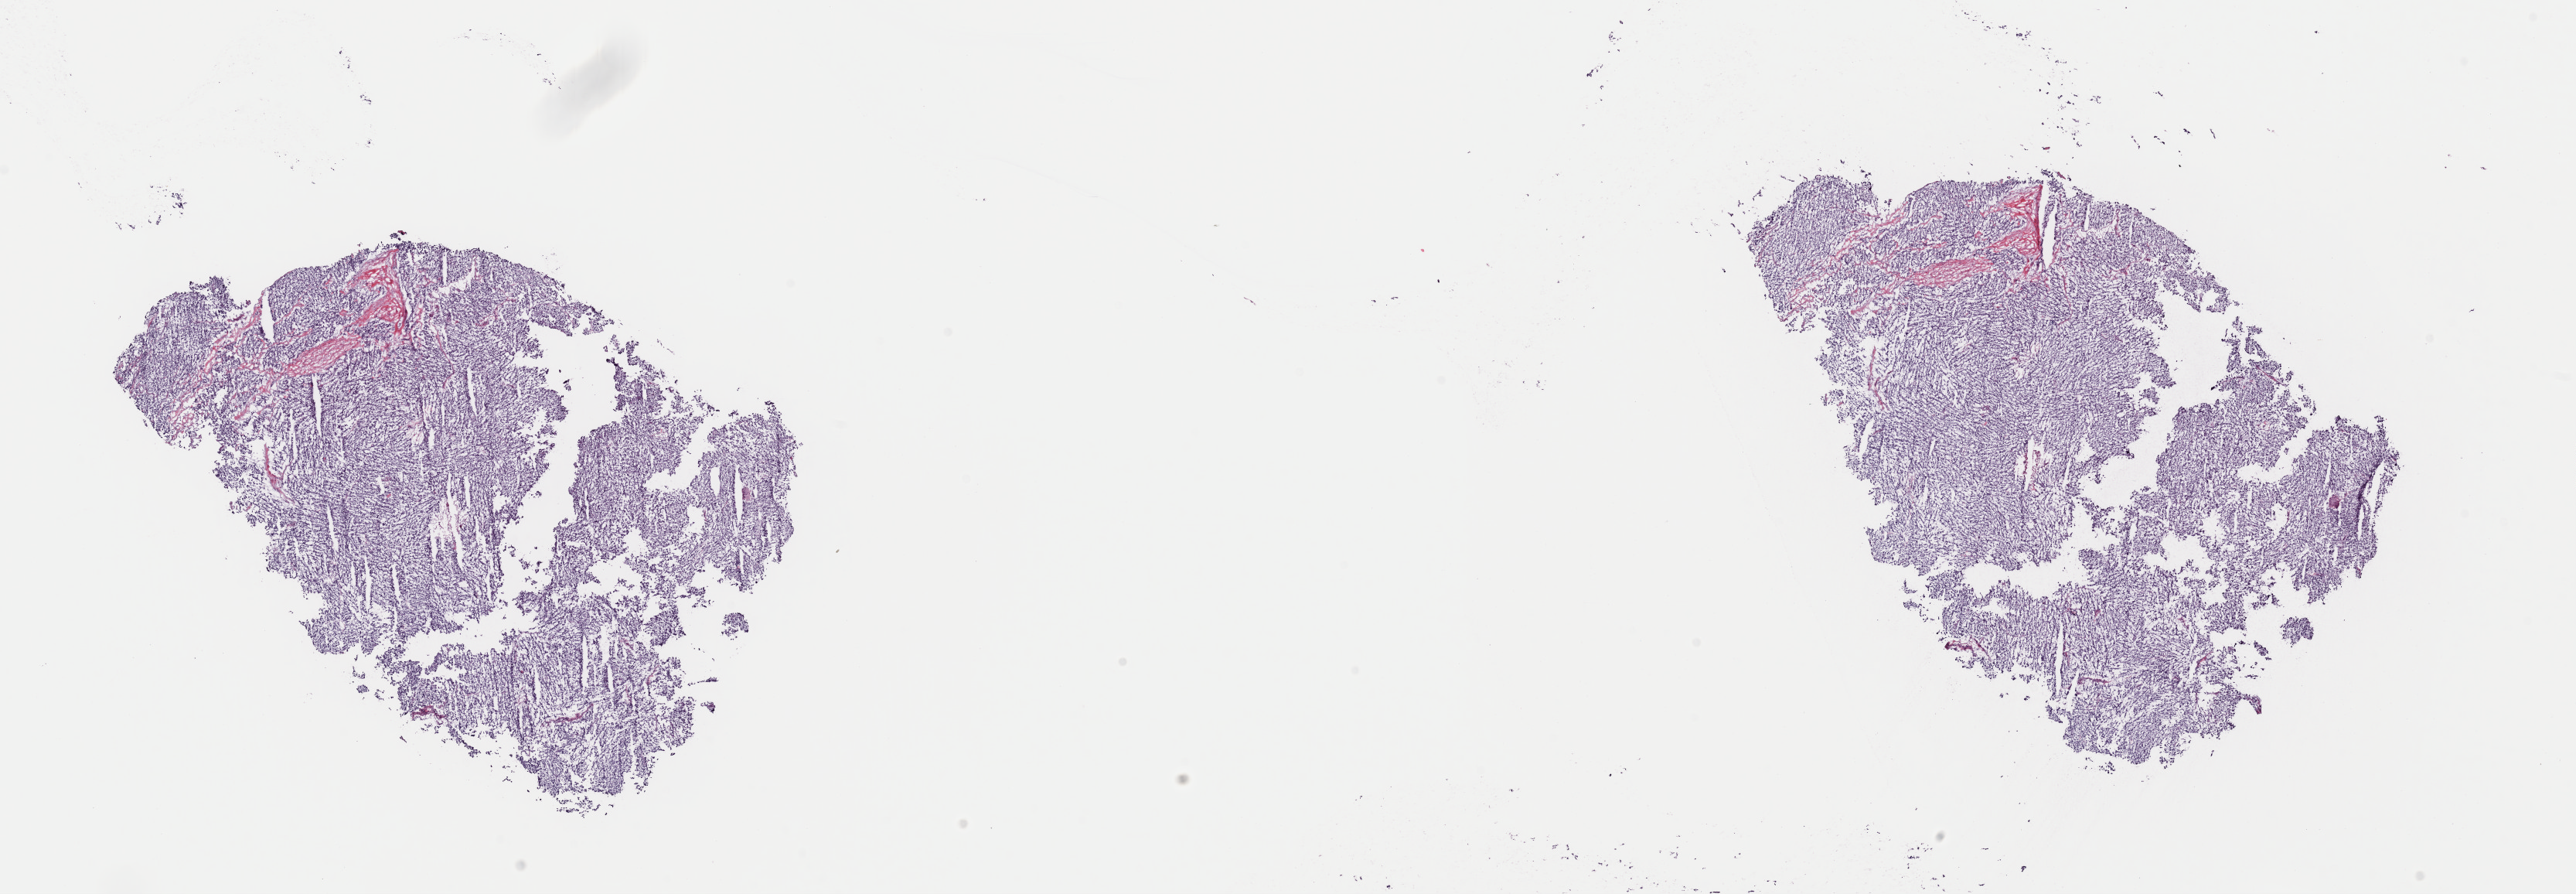
Digitized H&E tissue section (whole slide), a low-resolution overview of the entire scanned area, about 26.3 x 9.1 mm (slide scanned at 40x). Frozen section from the top of the tissue portion. Primary tumour sample from the adrenal gland. Female, age 30 years at initial diagnosis.
Pathologic diagnosis: Pheochromocytoma, NOS.